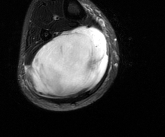
MRI of an extremity soft-tissue mass, one axial slice. Position 56 of 81 along the scan axis. T2-weighted fat-saturated. MR volume resampled by the dataset authors to the PET/CT grid (not the native acquisition matrix). 165 × 137 image matrix, field of view 161 × 134 mm. Male patient. Case-level facts recorded for this patient, not image findings: histological type: liposarcoma - round cell; grade: high; site of the primary tumour: right calf.
Structures marked on this image (expert contour drawn on MRI and transferred to this co-registered scan by the dataset authors):
- gross tumour volume (mass): bounding box <25,25,108,99> (left, top, right, bottom; pixels)